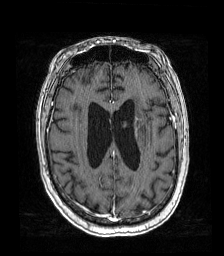
Brain MRI from a brain-tumour surgery series, one axial slice; position 64 of 192 along the scan axis; T1-weighted post-contrast; 1 mm slice thickness; 224 × 256 image matrix. Case-level facts recorded for this patient, not image findings: histopathology: Metastatic carcinoma from lung primary; tumour location: Left Frontal Caudate.
Outlined on this slice (expert manual segmentation):
- tumour: bounding box <119,117,128,135> (left, top, right, bottom; pixels)